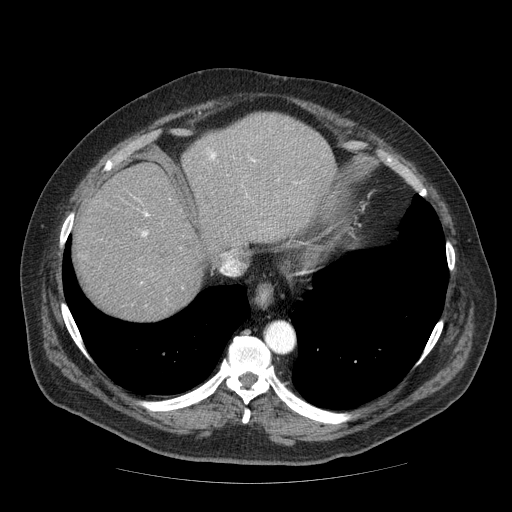
Contrast-enhanced abdominal CT (liver protocol), one axial slice. Slice 58 of 85 in the series (ordered by position). 120 kVp. Soft-tissue window (W 400 / L 40 HU). 2.5 mm slice thickness. 512 × 512 image matrix, field of view 420 × 420 mm. Case-level facts recorded for this patient, not image findings: diagnosis: hepatocellular carcinoma (patient treated with transarterial chemoembolisation; whether this scan precedes or follows treatment is not stated here); TNM stage (as recorded): Stage-IIIA; Child-Pugh class: A; tumour nodularity: multinodular; tumour size: 7 cm.
Annotated regions visible in this slice (semi-automatic segmentation, software-assisted and operator-edited):
- abdominal aorta: bounding box [x1, y1, x2, y2] px = [266, 324, 295, 353]
- liver parenchyma outside the tumour (the mass and vessels are separate outlines, so this box may not span the whole liver): [74, 112, 336, 320]
- liver vessels: [142, 153, 255, 236]